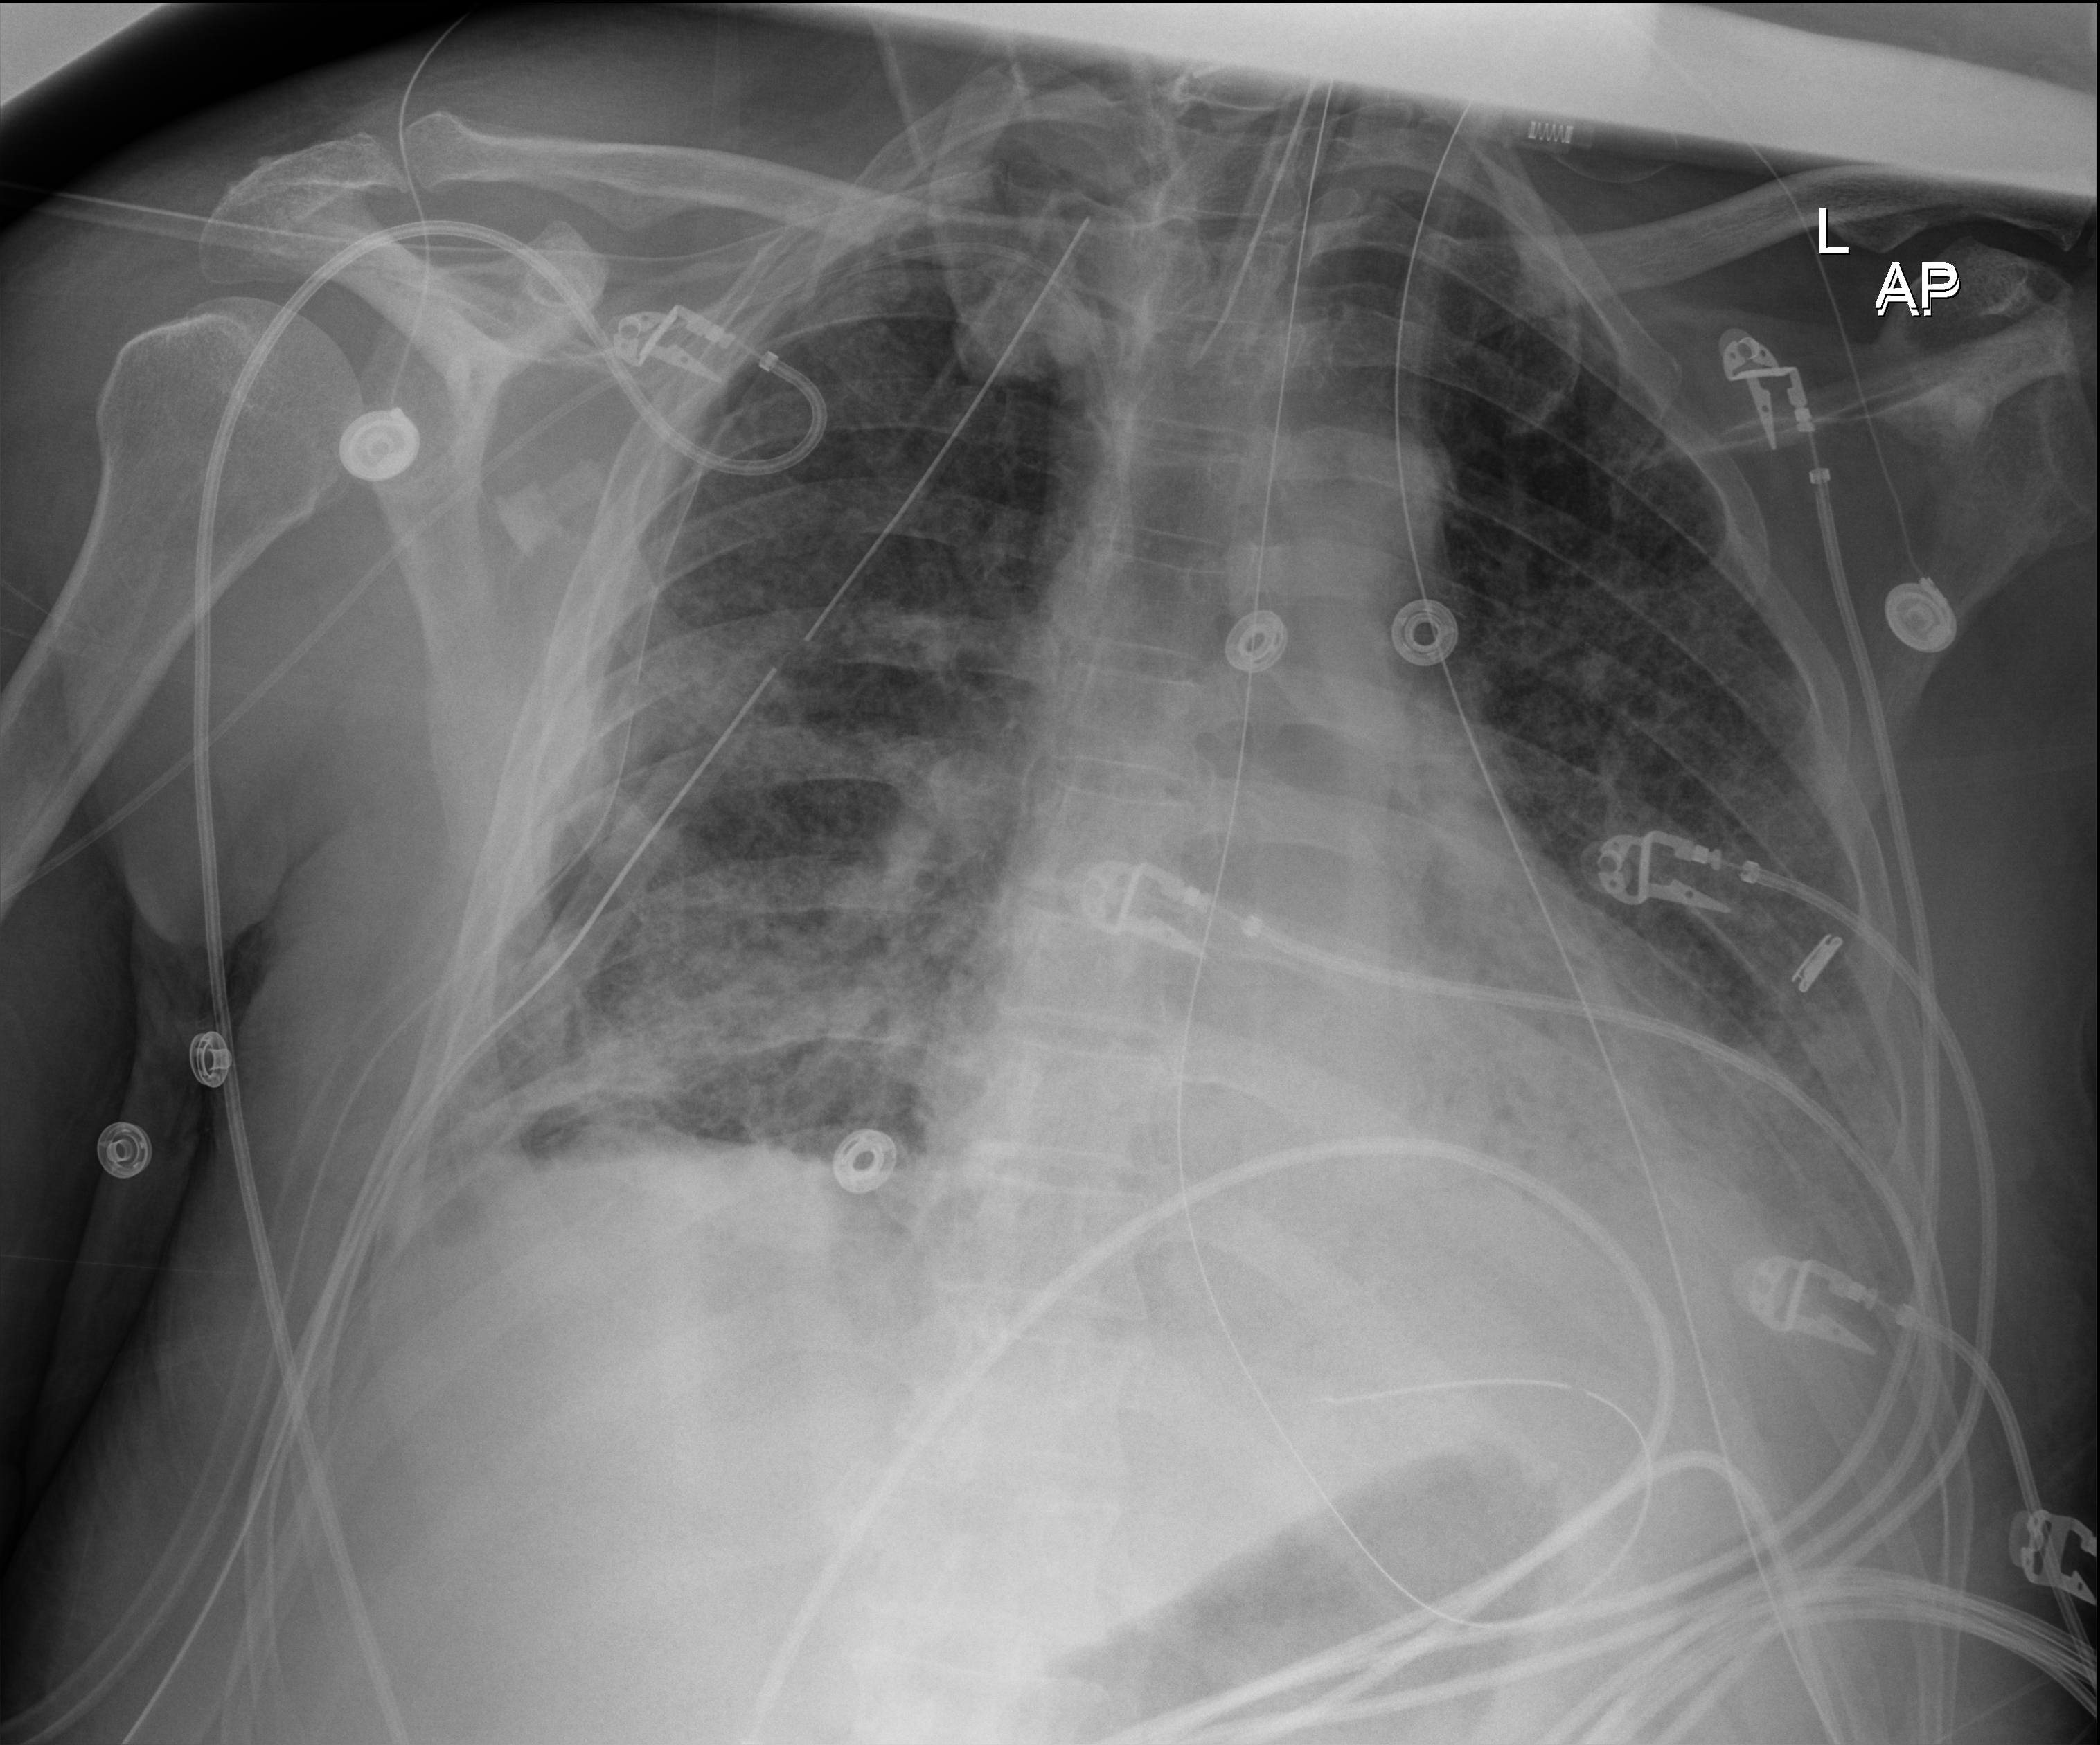
Chest X-ray (portable); anteroposterior (AP) projection. Male patient hospitalised with COVID-19, age 60–74 years.
From the hospital-stay record, not from the radiograph (when in the stay this image was taken is not recorded): admitted to intensive care during this hospital stay: yes.